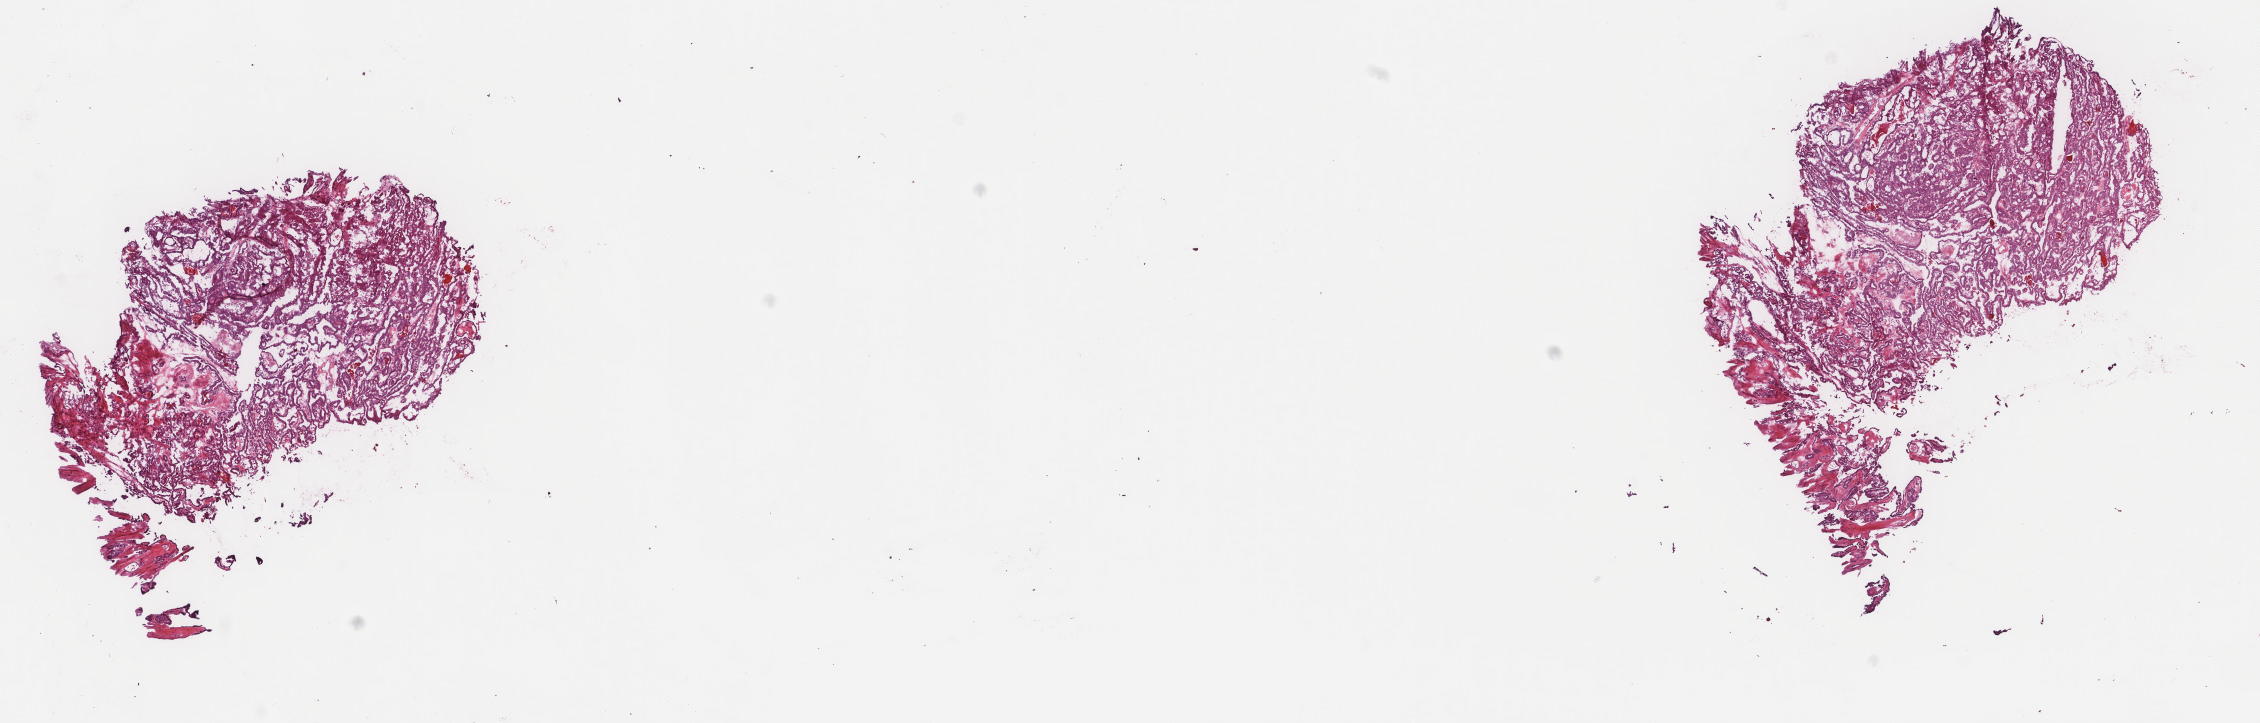
Whole-slide histology image, H&E — whole scanned area (about 17.9 x 5.7 mm, from a 40x scan) shown as a low-resolution overview, frozen section from the top of the tissue portion, thyroid, primary tumour sample. Male patient; age at initial diagnosis 66 years.
Diagnosis: Papillary adenocarcinoma, NOS (thyroid gland).